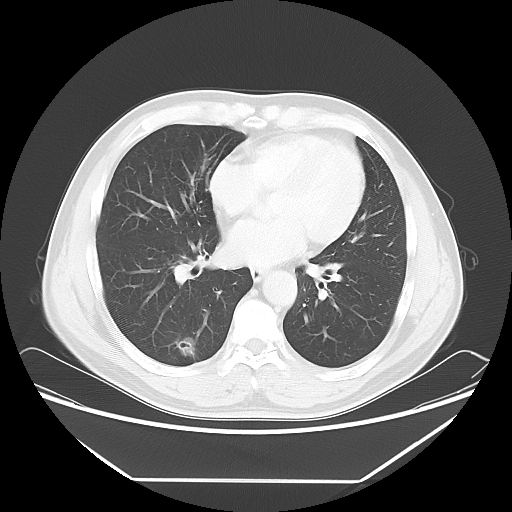
Chest CT, one axial slice; slice 29 of 65 in the series (ordered by position); reconstruction kernel LUNG; lung window (W 1500 / L -600 HU); 5 mm slice thickness; 512 × 512 image matrix, field of view 418 × 418 mm. Male patient, age 50 years. Case-level facts recorded for this patient, not image findings: clinical TNM (as recorded): T1c N0 M0; histopathological grade: G3.
Outlined on this slice (bounding box drawn by a radiologist):
- lung tumour (recorded histology: adenocarcinoma): box from (x=172, y=333) to (x=201, y=364) px